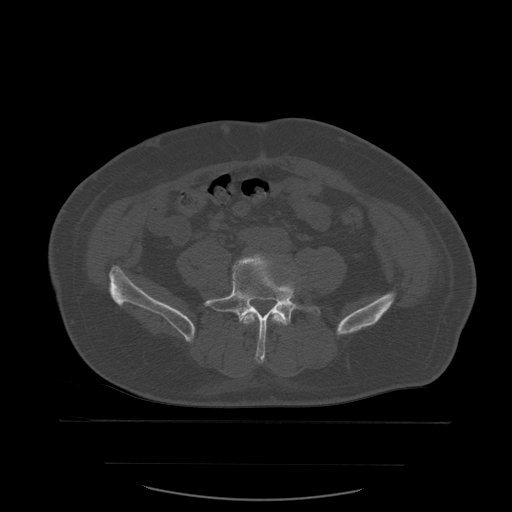
CT including the spine, one axial slice; position 145 of 590 along the scan axis; bone window (W 1800 / L 400 HU); 512 × 512 image matrix. Patient age 71 years. From the clinical record (not read from this slice): primary cancer: lung; vertebrae with lytic lesions (as recorded): T1, T2, L5, S1.
Outlined on this slice (semi-automatically segmented with operator editing):
- L4 vertebra: bounding box (x1, y1, x2, y2) in pixels: (241, 313, 282, 325)
- L5 vertebra: (204, 254, 322, 363)